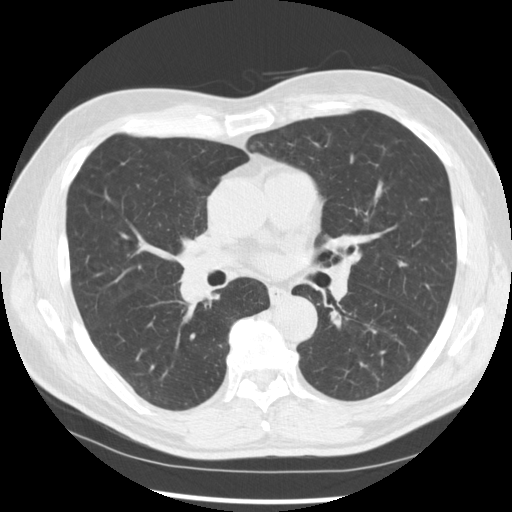
Low-dose screening chest CT, one axial slice. Slice 154 of 277 in the series (ordered by position). Lung window (W 1500 / L -600 HU). 512 × 512 image matrix, field of view 365 × 365 mm.
Annotated regions visible in this slice (manually delineated by an expert):
- lesion 1 (tumor, middle lobe of right lung): bounding box [x1, y1, x2, y2] px = [178, 269, 210, 305]